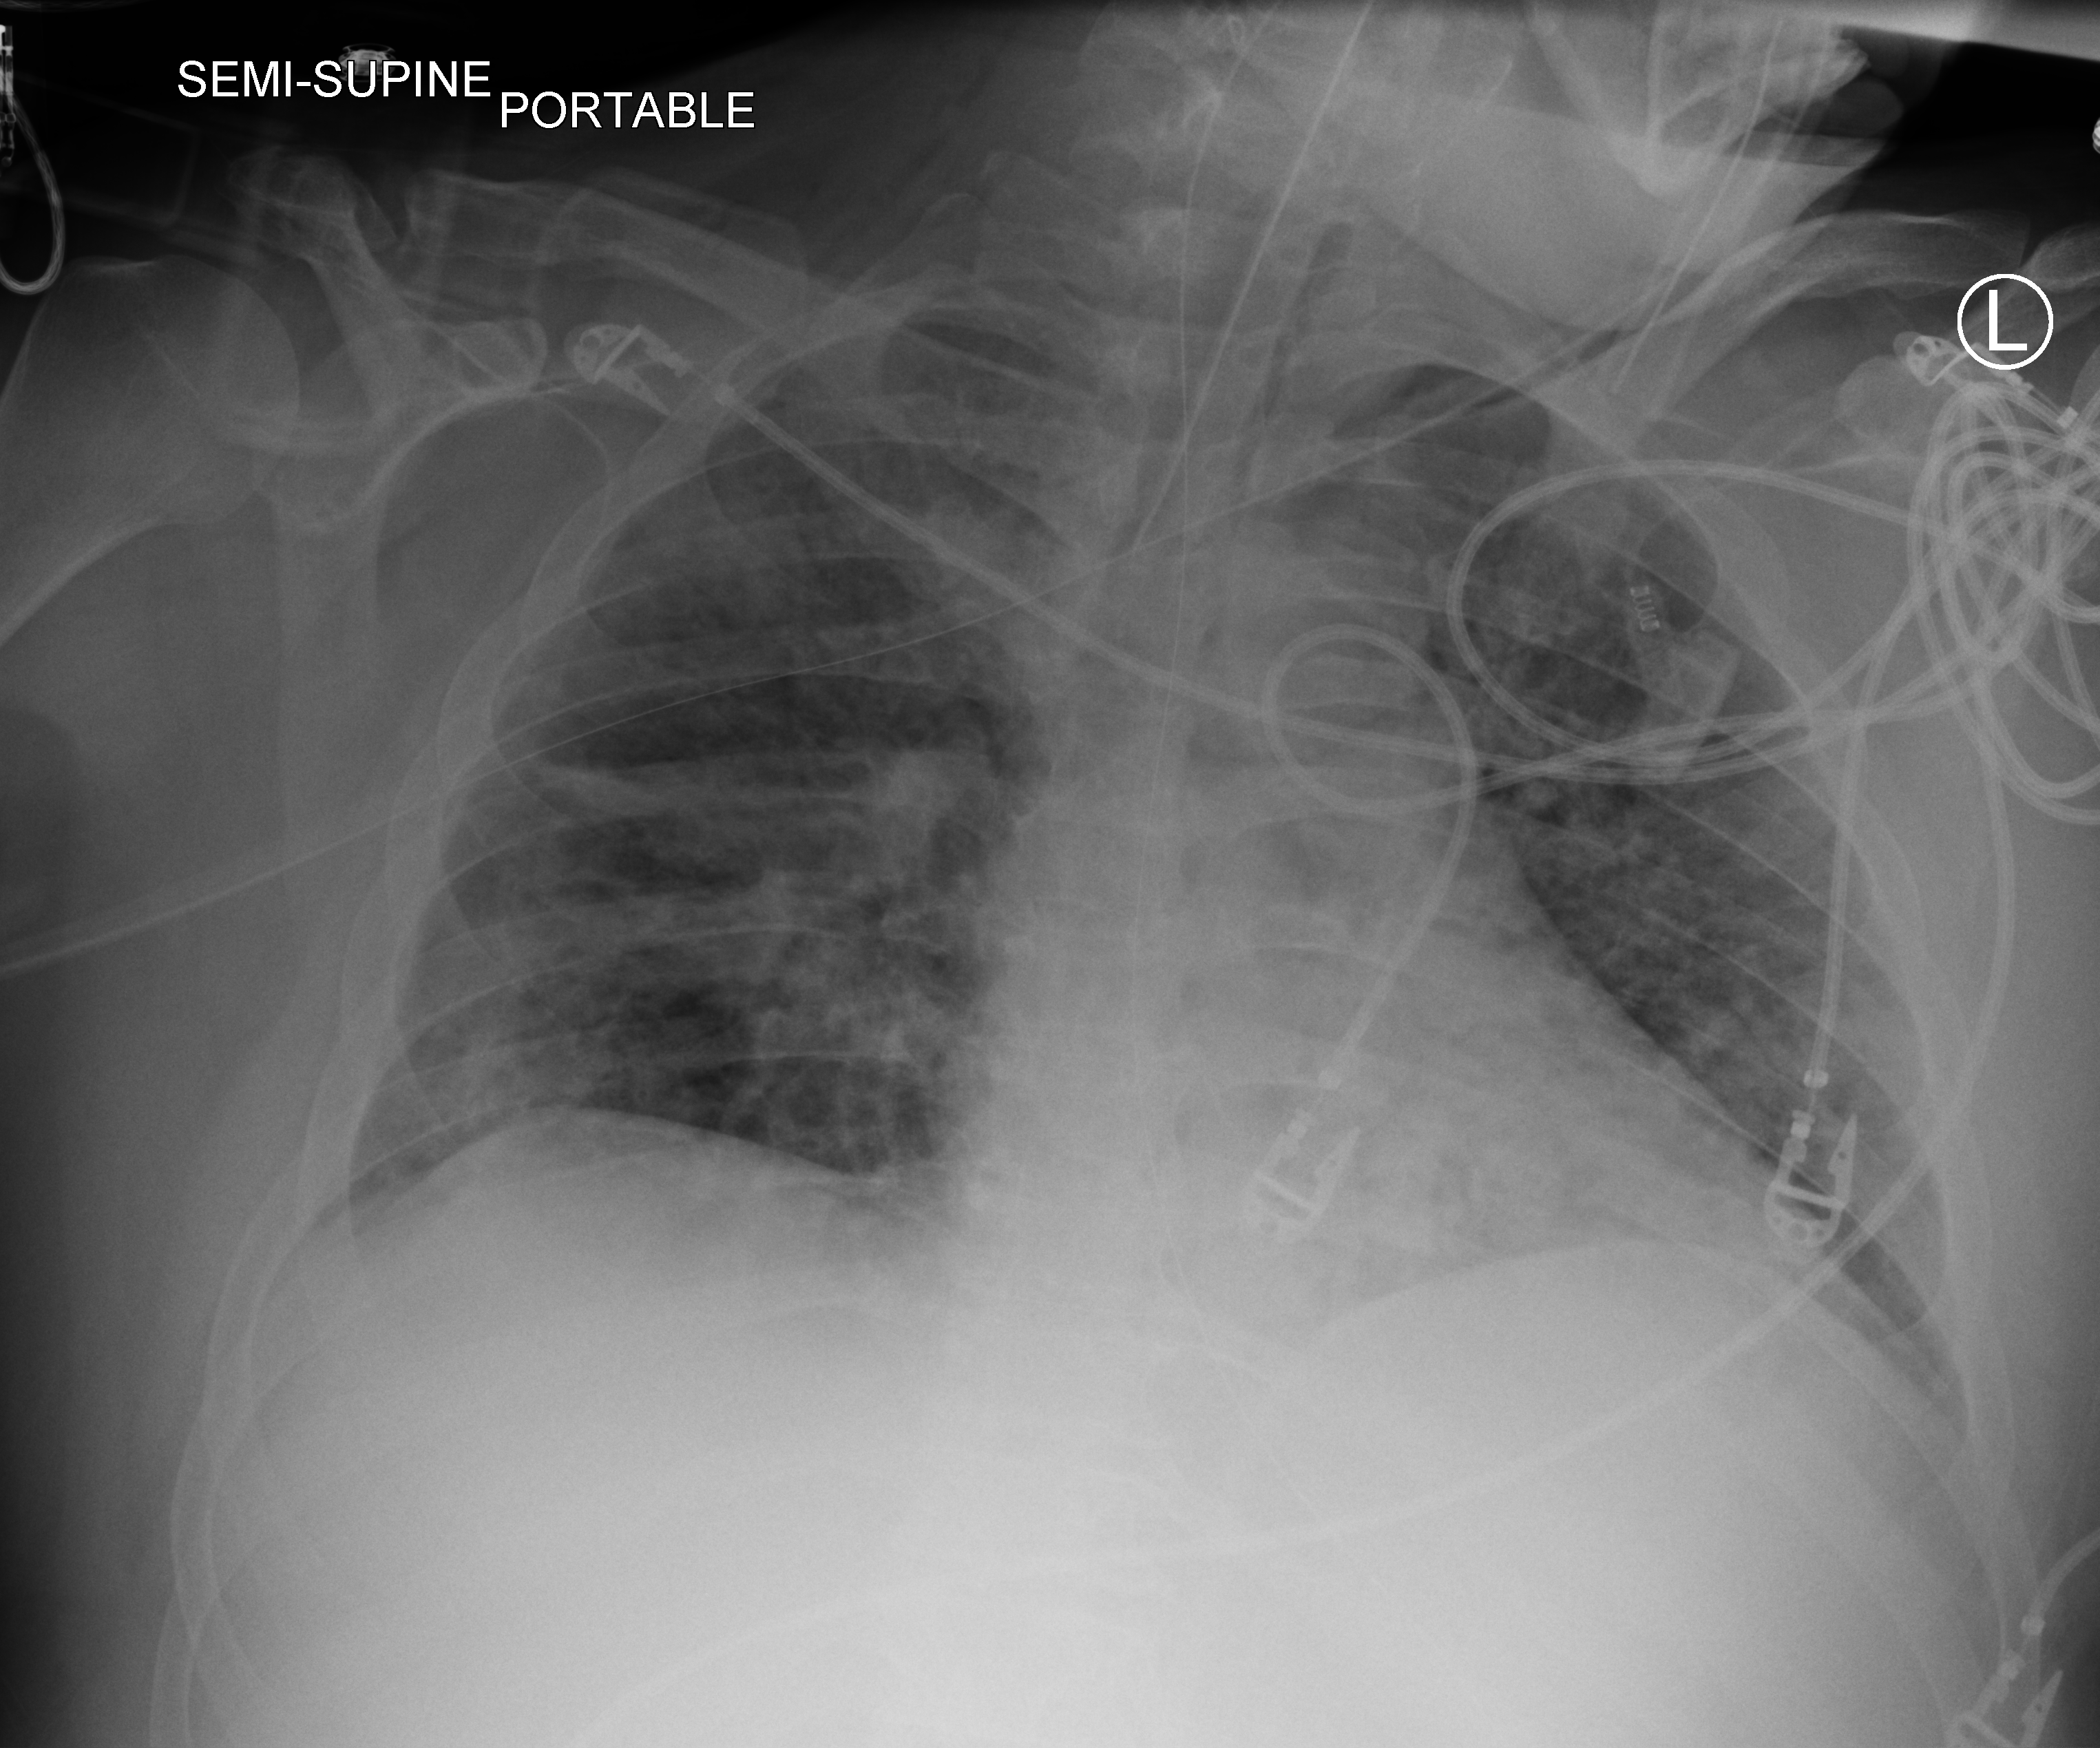
Chest X-ray (portable). Adult patient hospitalised with COVID-19, age 18–59 years.
Hospital-stay facts (about this admission, not read from this image; timing relative to this image not recorded): mechanically ventilated during this hospital stay: yes.